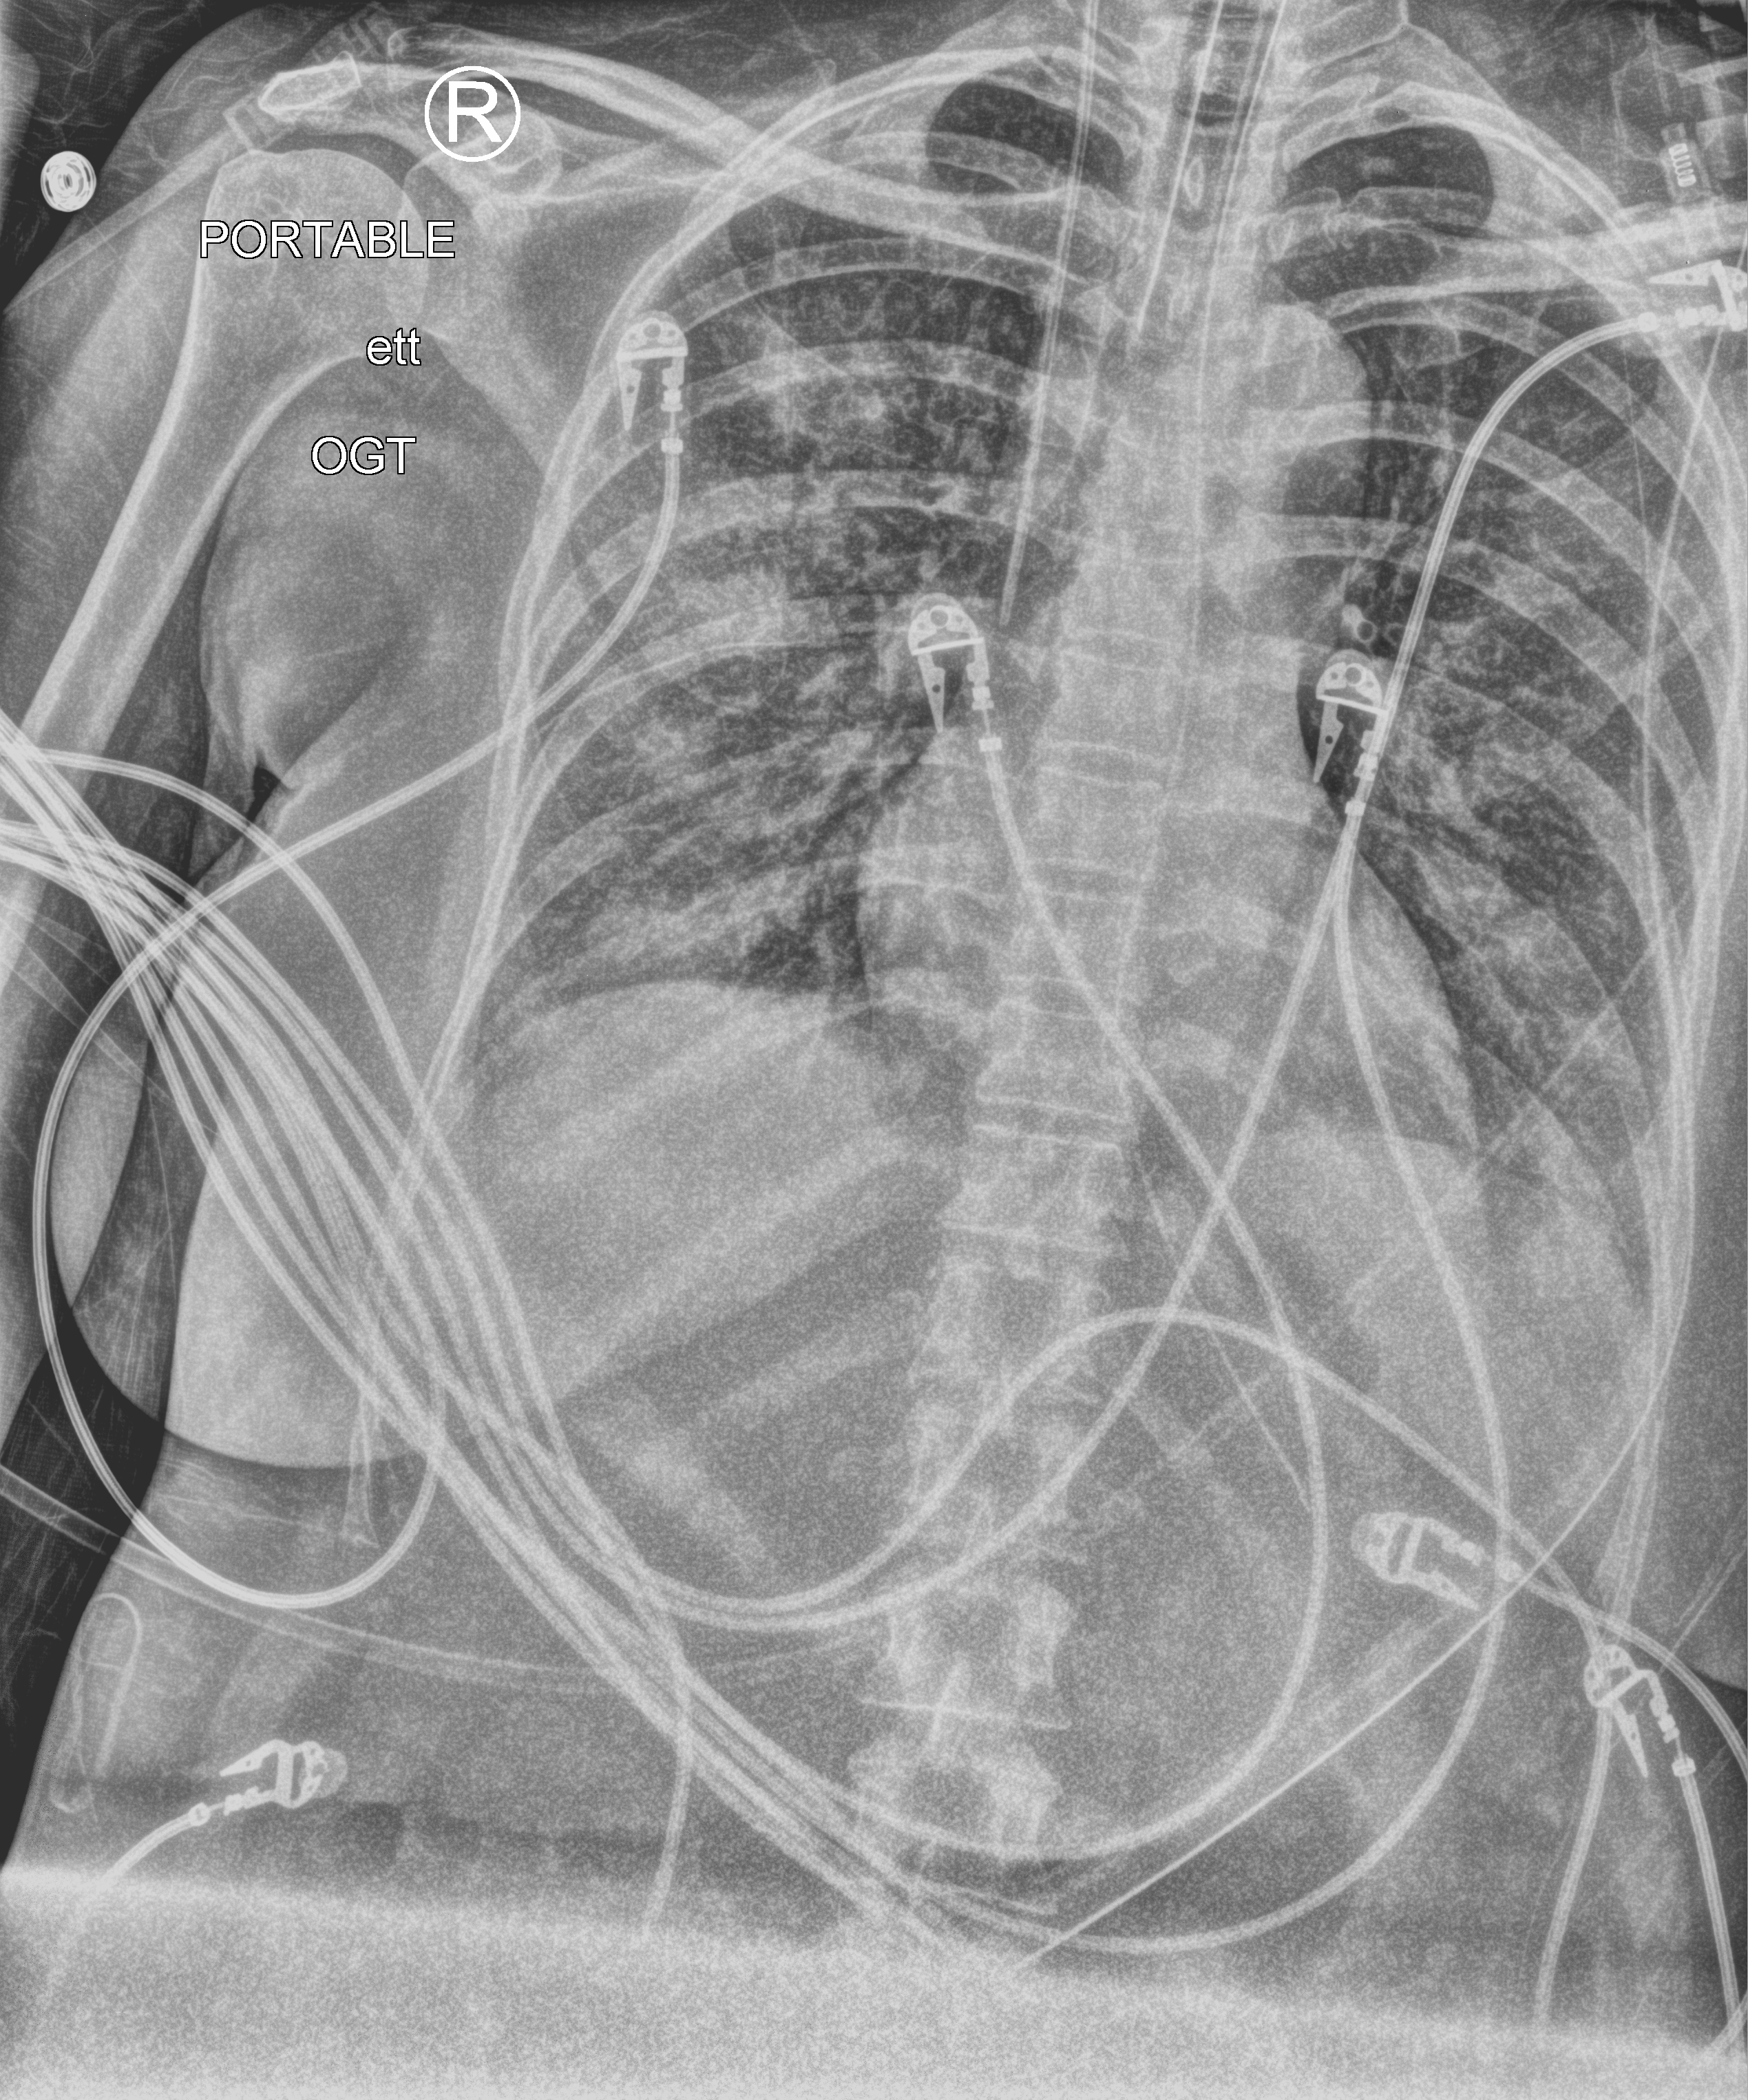
Bedside chest radiograph (computed radiography); anteroposterior (AP) projection. Female patient hospitalised with COVID-19, age 18–59 years.
Hospital-stay facts (about this admission, not read from this image; timing relative to this image not recorded): chronic kidney disease (admission record): no; mechanically ventilated during this hospital stay: yes.